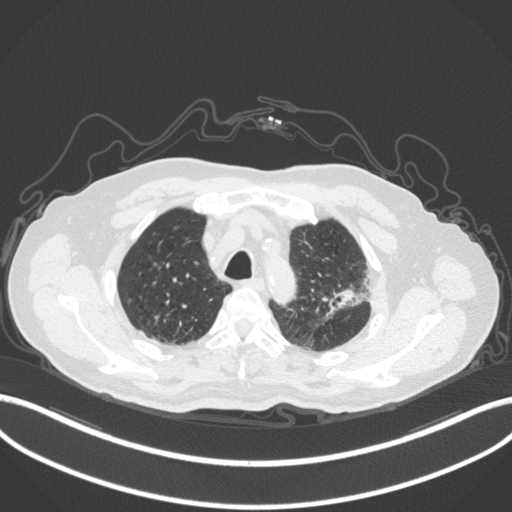
Chest CT, one axial slice. Slice 244 of 331 in the series (ordered by position). Reconstruction kernel B31f. Lung window (W 1500 / L -600 HU). 1 mm slice thickness. 512 × 512 image matrix. Male patient, age 79 years. From the clinical record (not read from this slice): clinical TNM (as recorded): T2a N1 M1; histopathological grade: G3.
Outlined on this slice (bounding box drawn by a radiologist):
- lung tumour (recorded histology: adenocarcinoma): bounding box (x1, y1, x2, y2) in pixels: (320, 276, 372, 325)